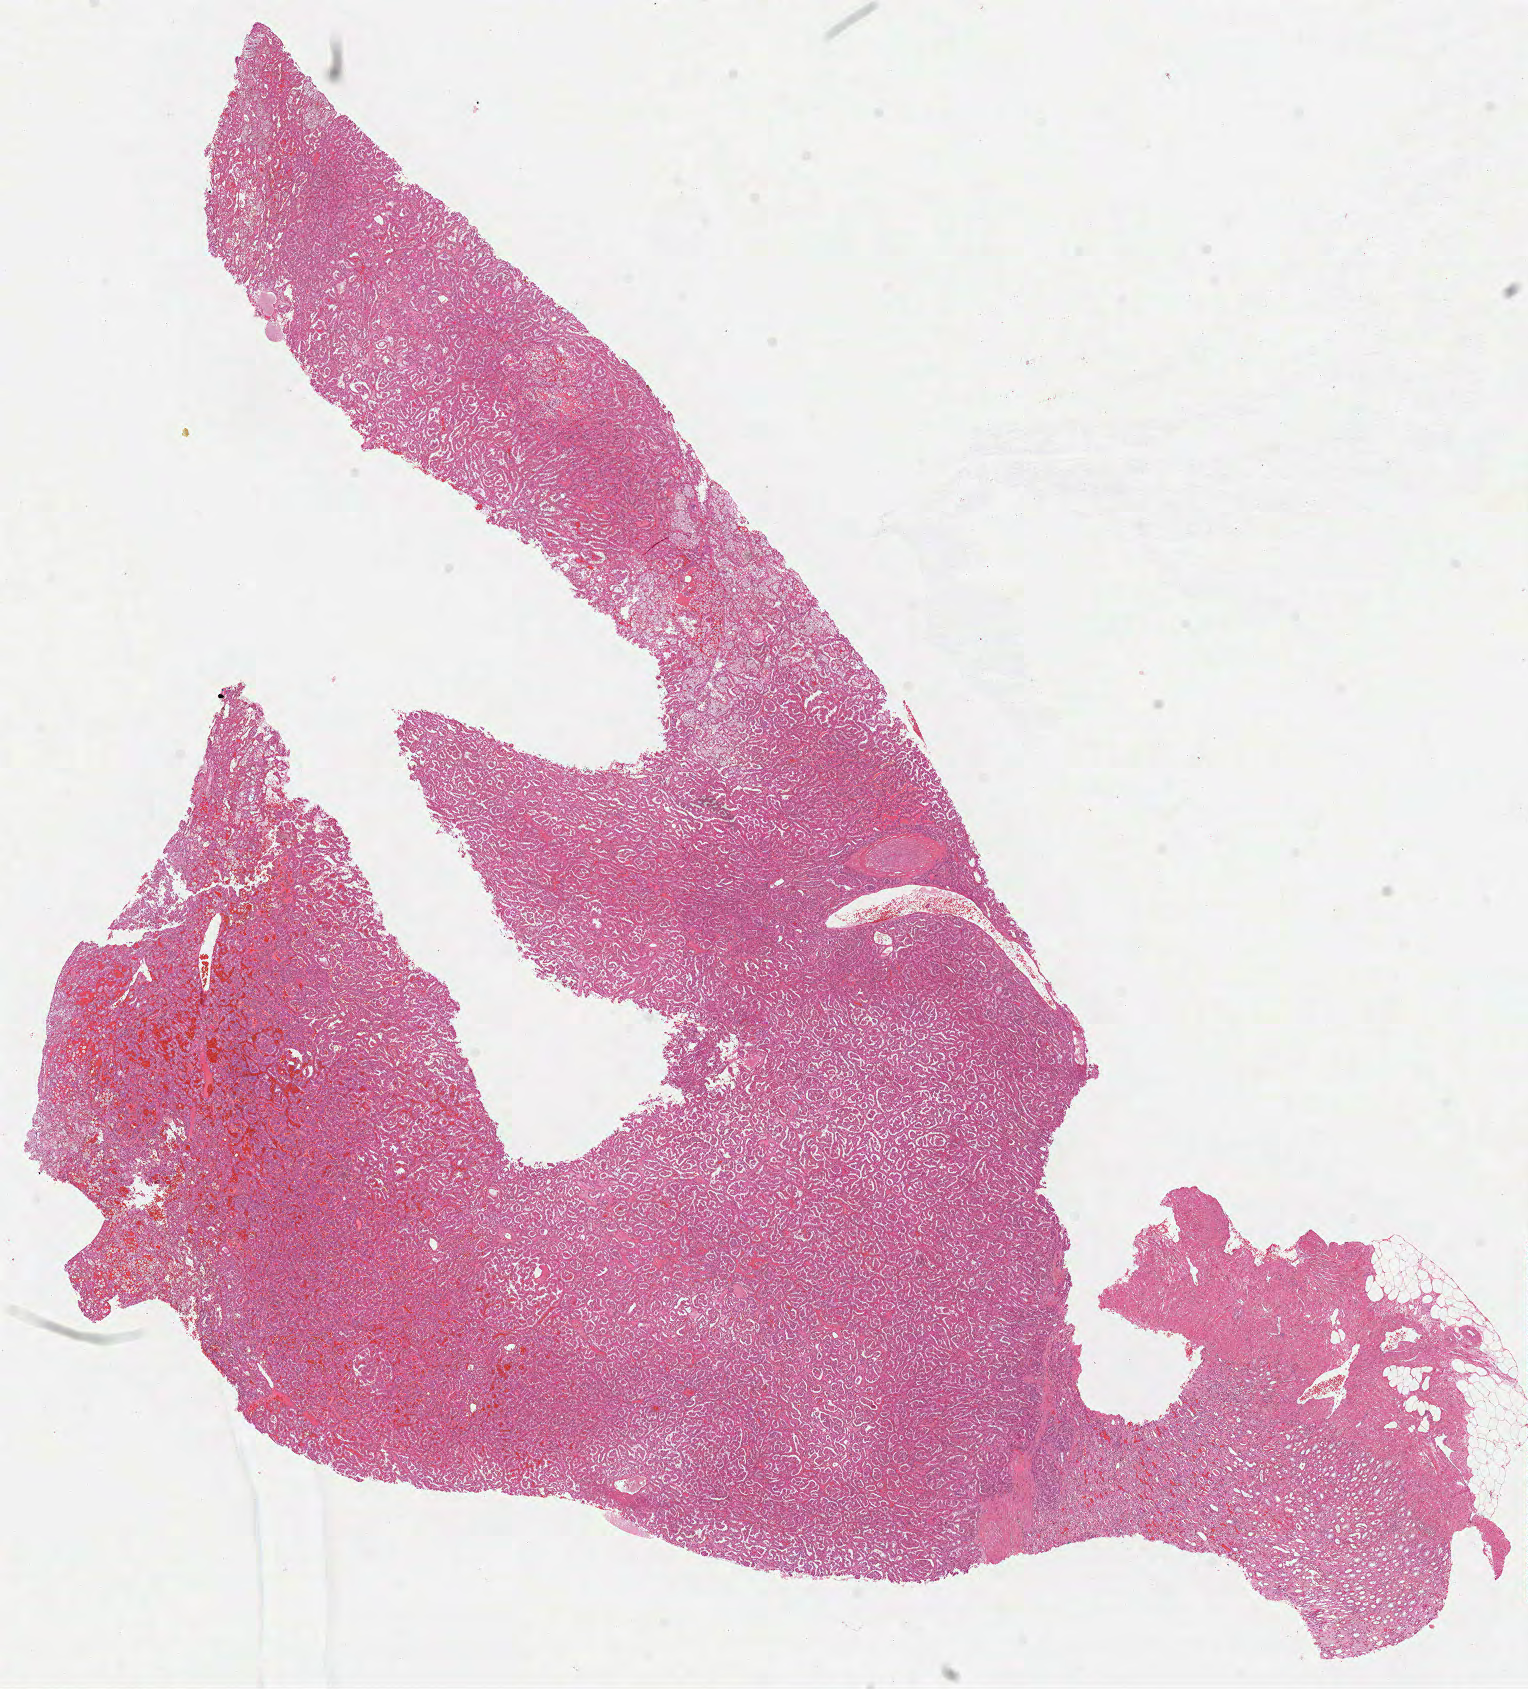
Whole-slide histology image, H&E, a low-resolution overview of the entire scanned area, about 12.3 x 13.6 mm (from a 40x scan); formalin-fixed paraffin-embedded (FFPE) diagnostic section; primary tumour sample from the kidney. Female patient; age at initial diagnosis 71 years.
TNM: T1b NX MX. Pathologic diagnosis: Papillary adenocarcinoma, NOS. AJCC pathologic stage: I.